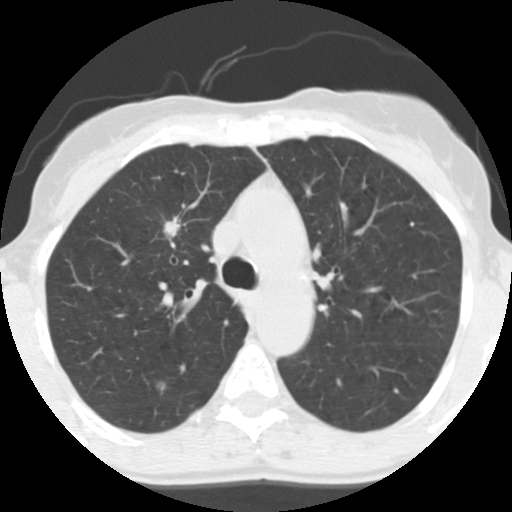
Low-dose screening chest CT, axial slice; baseline annual screen; lung window (W 1500 / L -600 HU); standard (soft-tissue) reconstruction kernel (STANDARD); slice 45 of 130 in the series. Female, age 56 years at enrolment.
• Lesion marked by an expert reader, bounding box <151,209,193,248> (left, top, right, bottom; pixels).
• Screening reader's record for this exam (one nodule recorded; not confirmed to be the boxed lesion): non-calcified nodule or mass ≥4 mm, right upper lobe, 12 × 9 mm, spiculated (stellate) margins, soft tissue attenuation.
• Participant outcome: lung cancer diagnosed 779 days after this screen (after the third annual screen) — adenocarcinoma, NOS, right upper lobe, moderately differentiated (G2), stage IA (AJCC 6th edition), 19 mm at pathology.